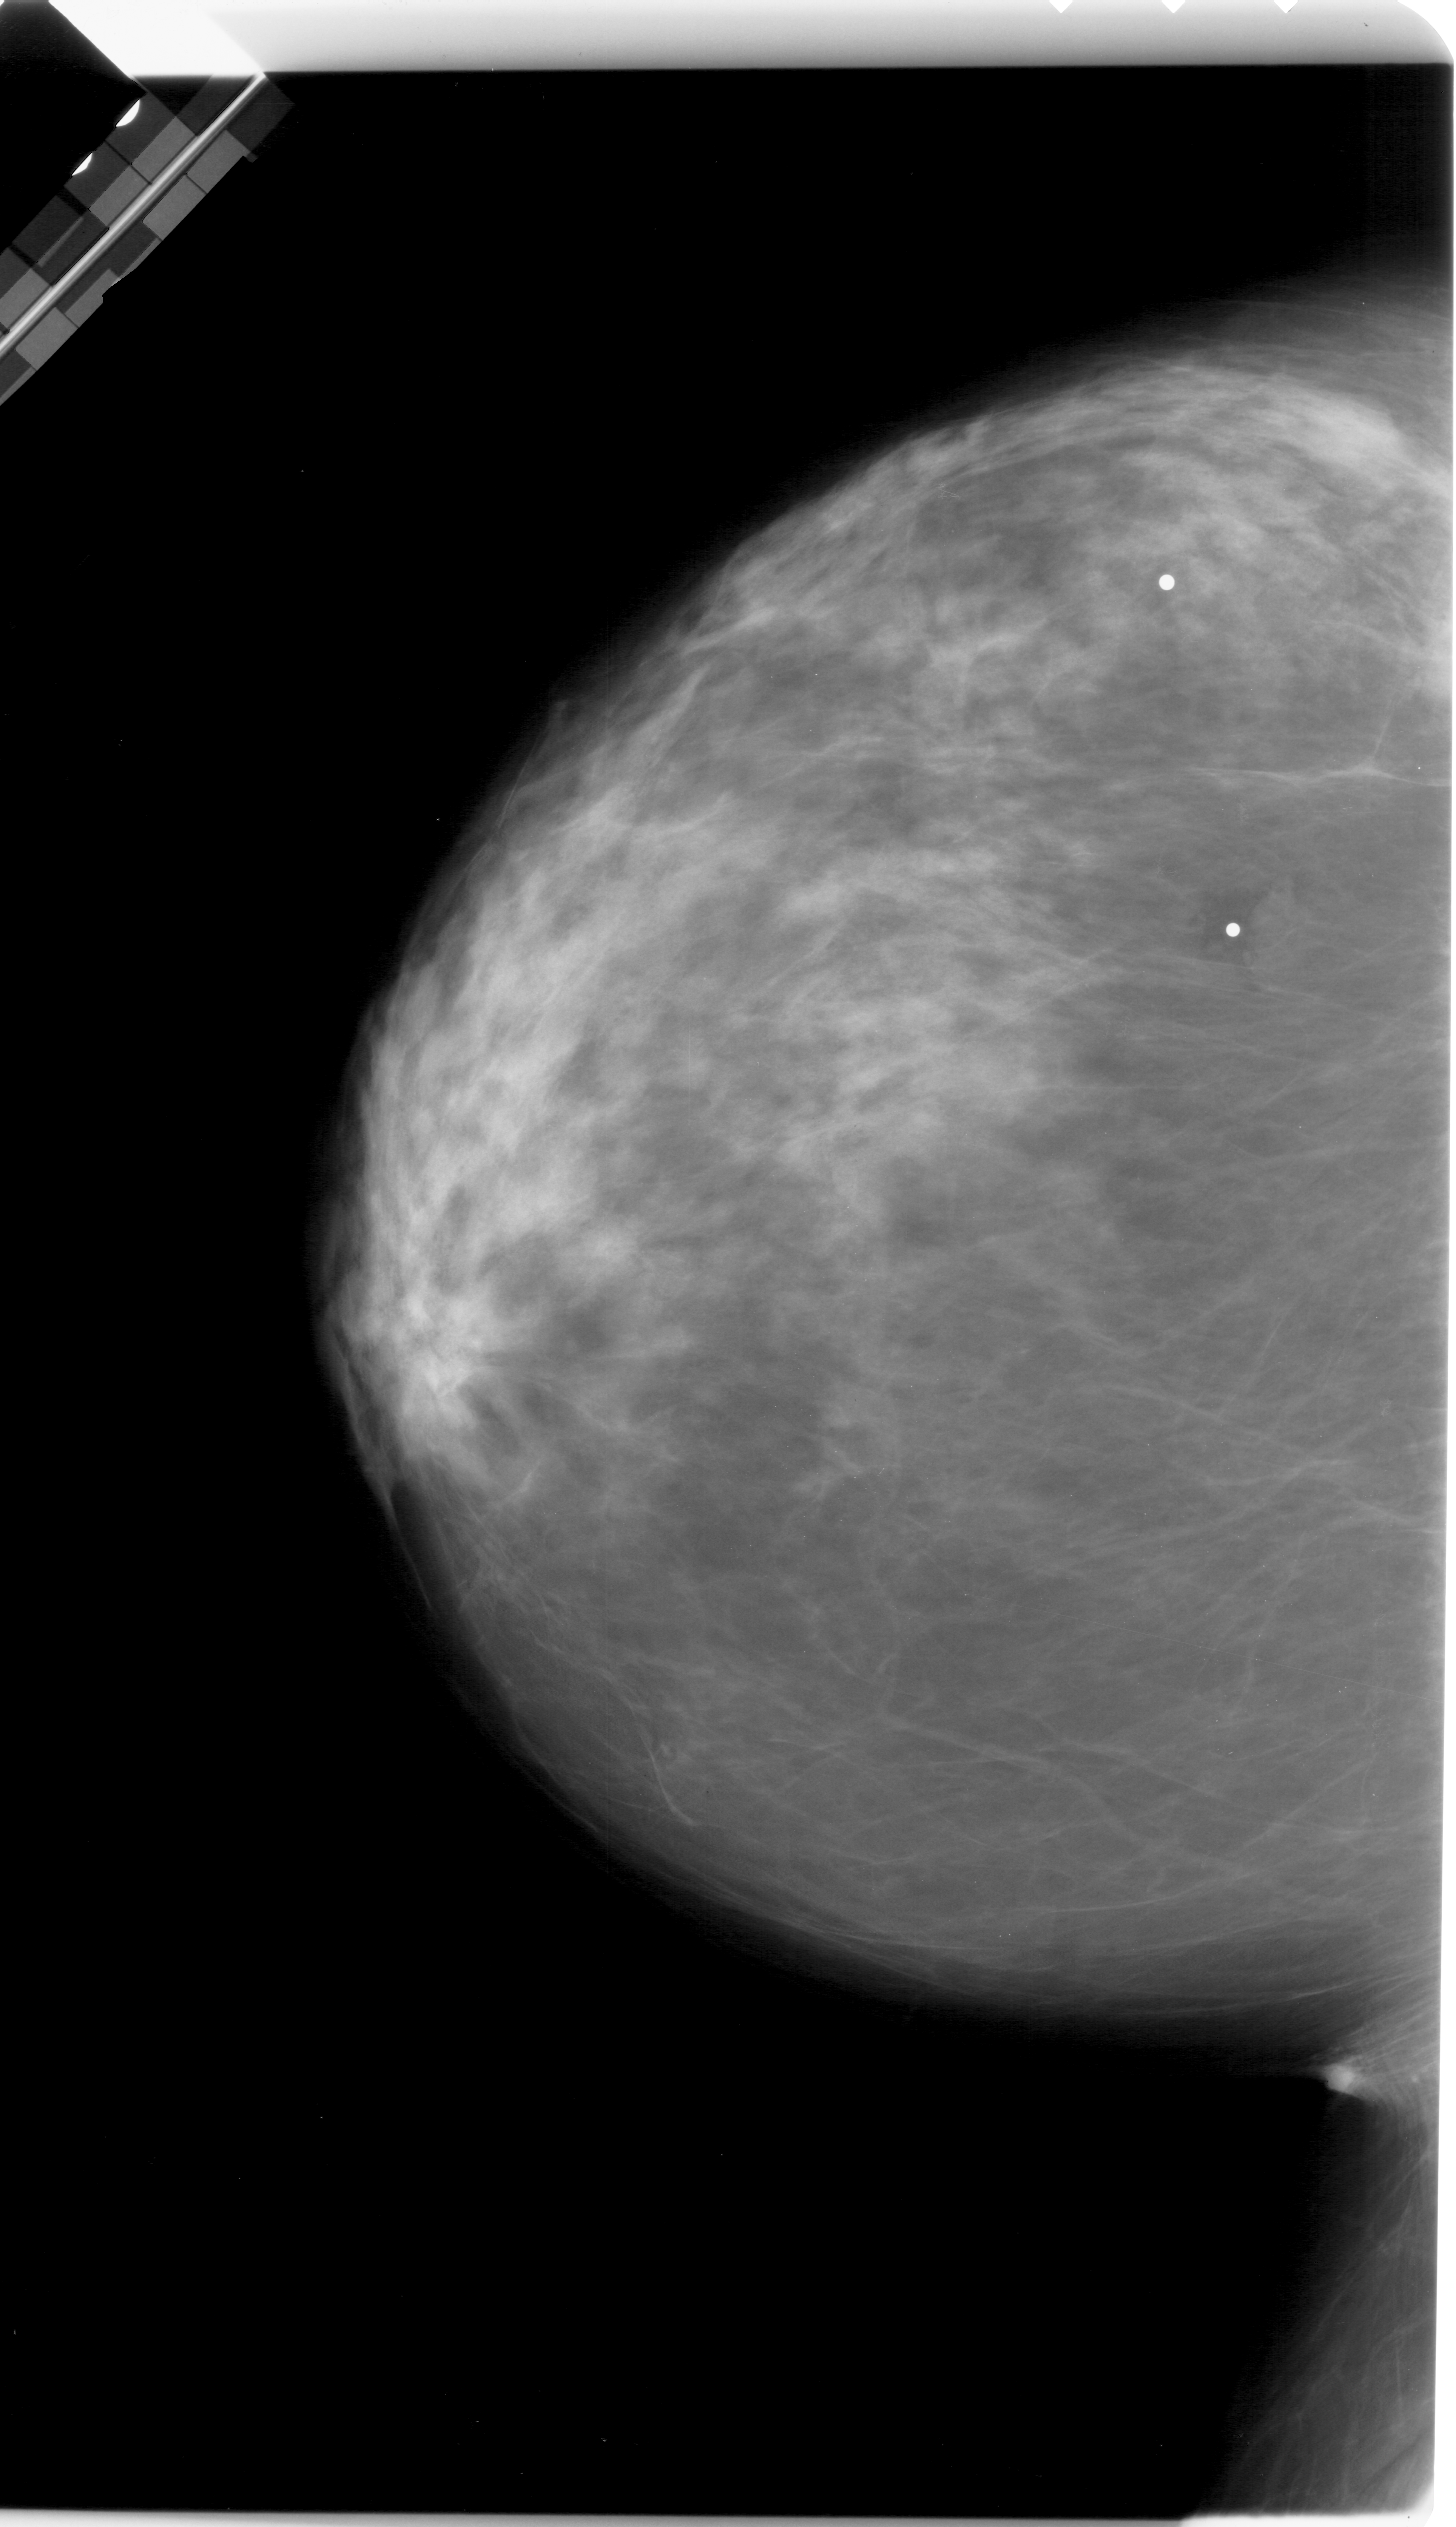
Digitized screen-film mammogram; left breast; craniocaudal (CC) view; BI-RADS breast density category 3 (scale 1–4).
Radiologist-marked abnormalities on this image: mass, shape lobulated, margins obscured; BI-RADS assessment category 4; pathology result (as recorded, not read from the image): malignant.